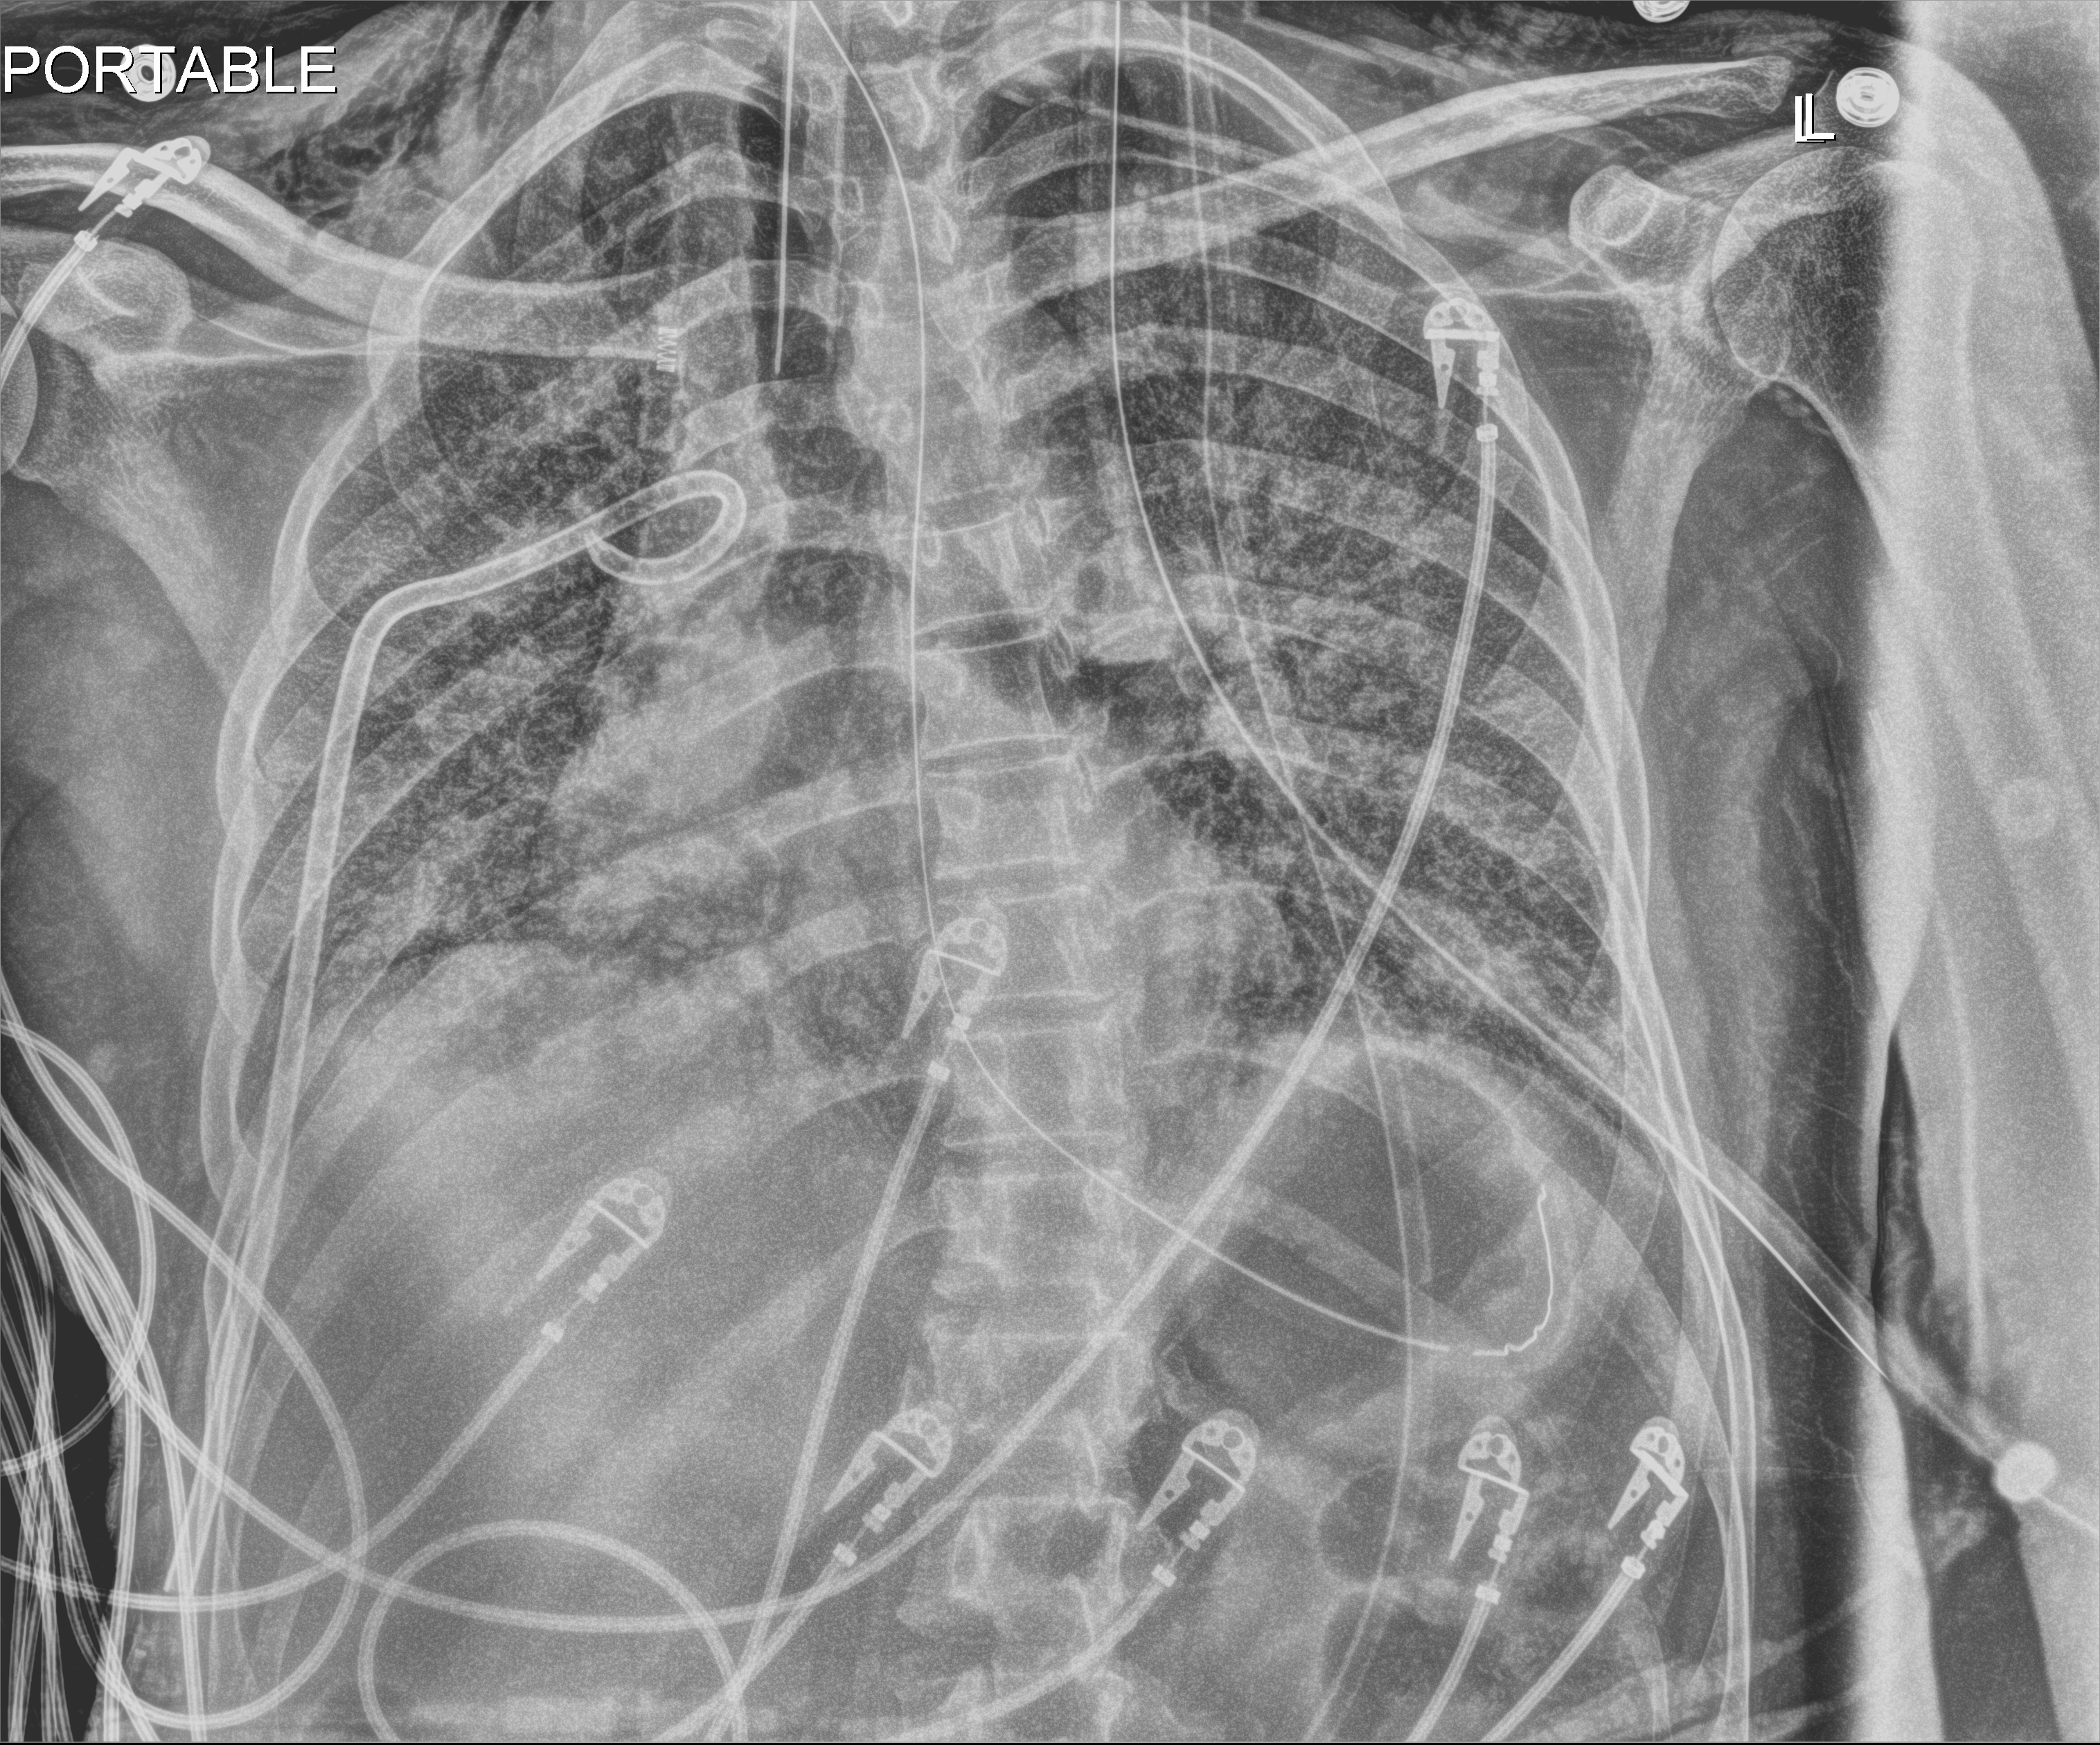
Portable chest radiograph, anteroposterior (AP) projection. Patient hospitalised with COVID-19, aged 18–59 years.
Hospital-stay facts (about this admission, not read from this image; timing relative to this image not recorded): mechanically ventilated during this hospital stay: yes.